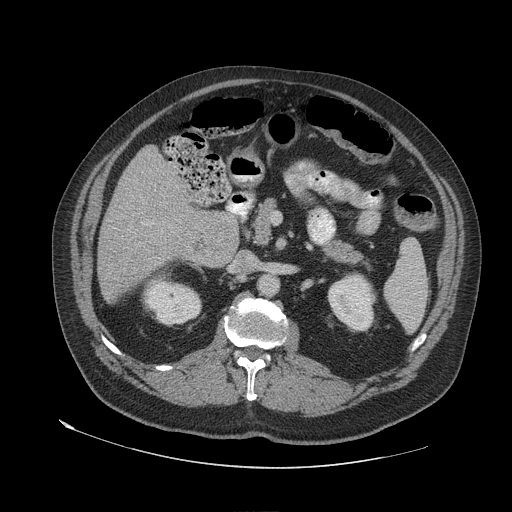
Contrast-enhanced abdominal CT (liver protocol), one axial slice; slice 24 of 79 in the series (ordered by position); 140 kVp; soft-tissue window (W 400 / L 40 HU); 2.5 mm slice thickness; 512 × 512 image matrix. Case-level facts recorded for this patient, not image findings: diagnosis: hepatocellular carcinoma (patient treated with transarterial chemoembolisation; whether this scan precedes or follows treatment is not stated here); TNM stage (as recorded): Stage-IVA; Child-Pugh class: A; tumour differentiation: well differentiated.
Annotated regions visible in this slice (semi-automatic segmentation, software-assisted and operator-edited):
- liver parenchyma outside the tumour (the mass and vessels are separate outlines, so this box may not span the whole liver): bounding box <97,146,238,301> (left, top, right, bottom; pixels)